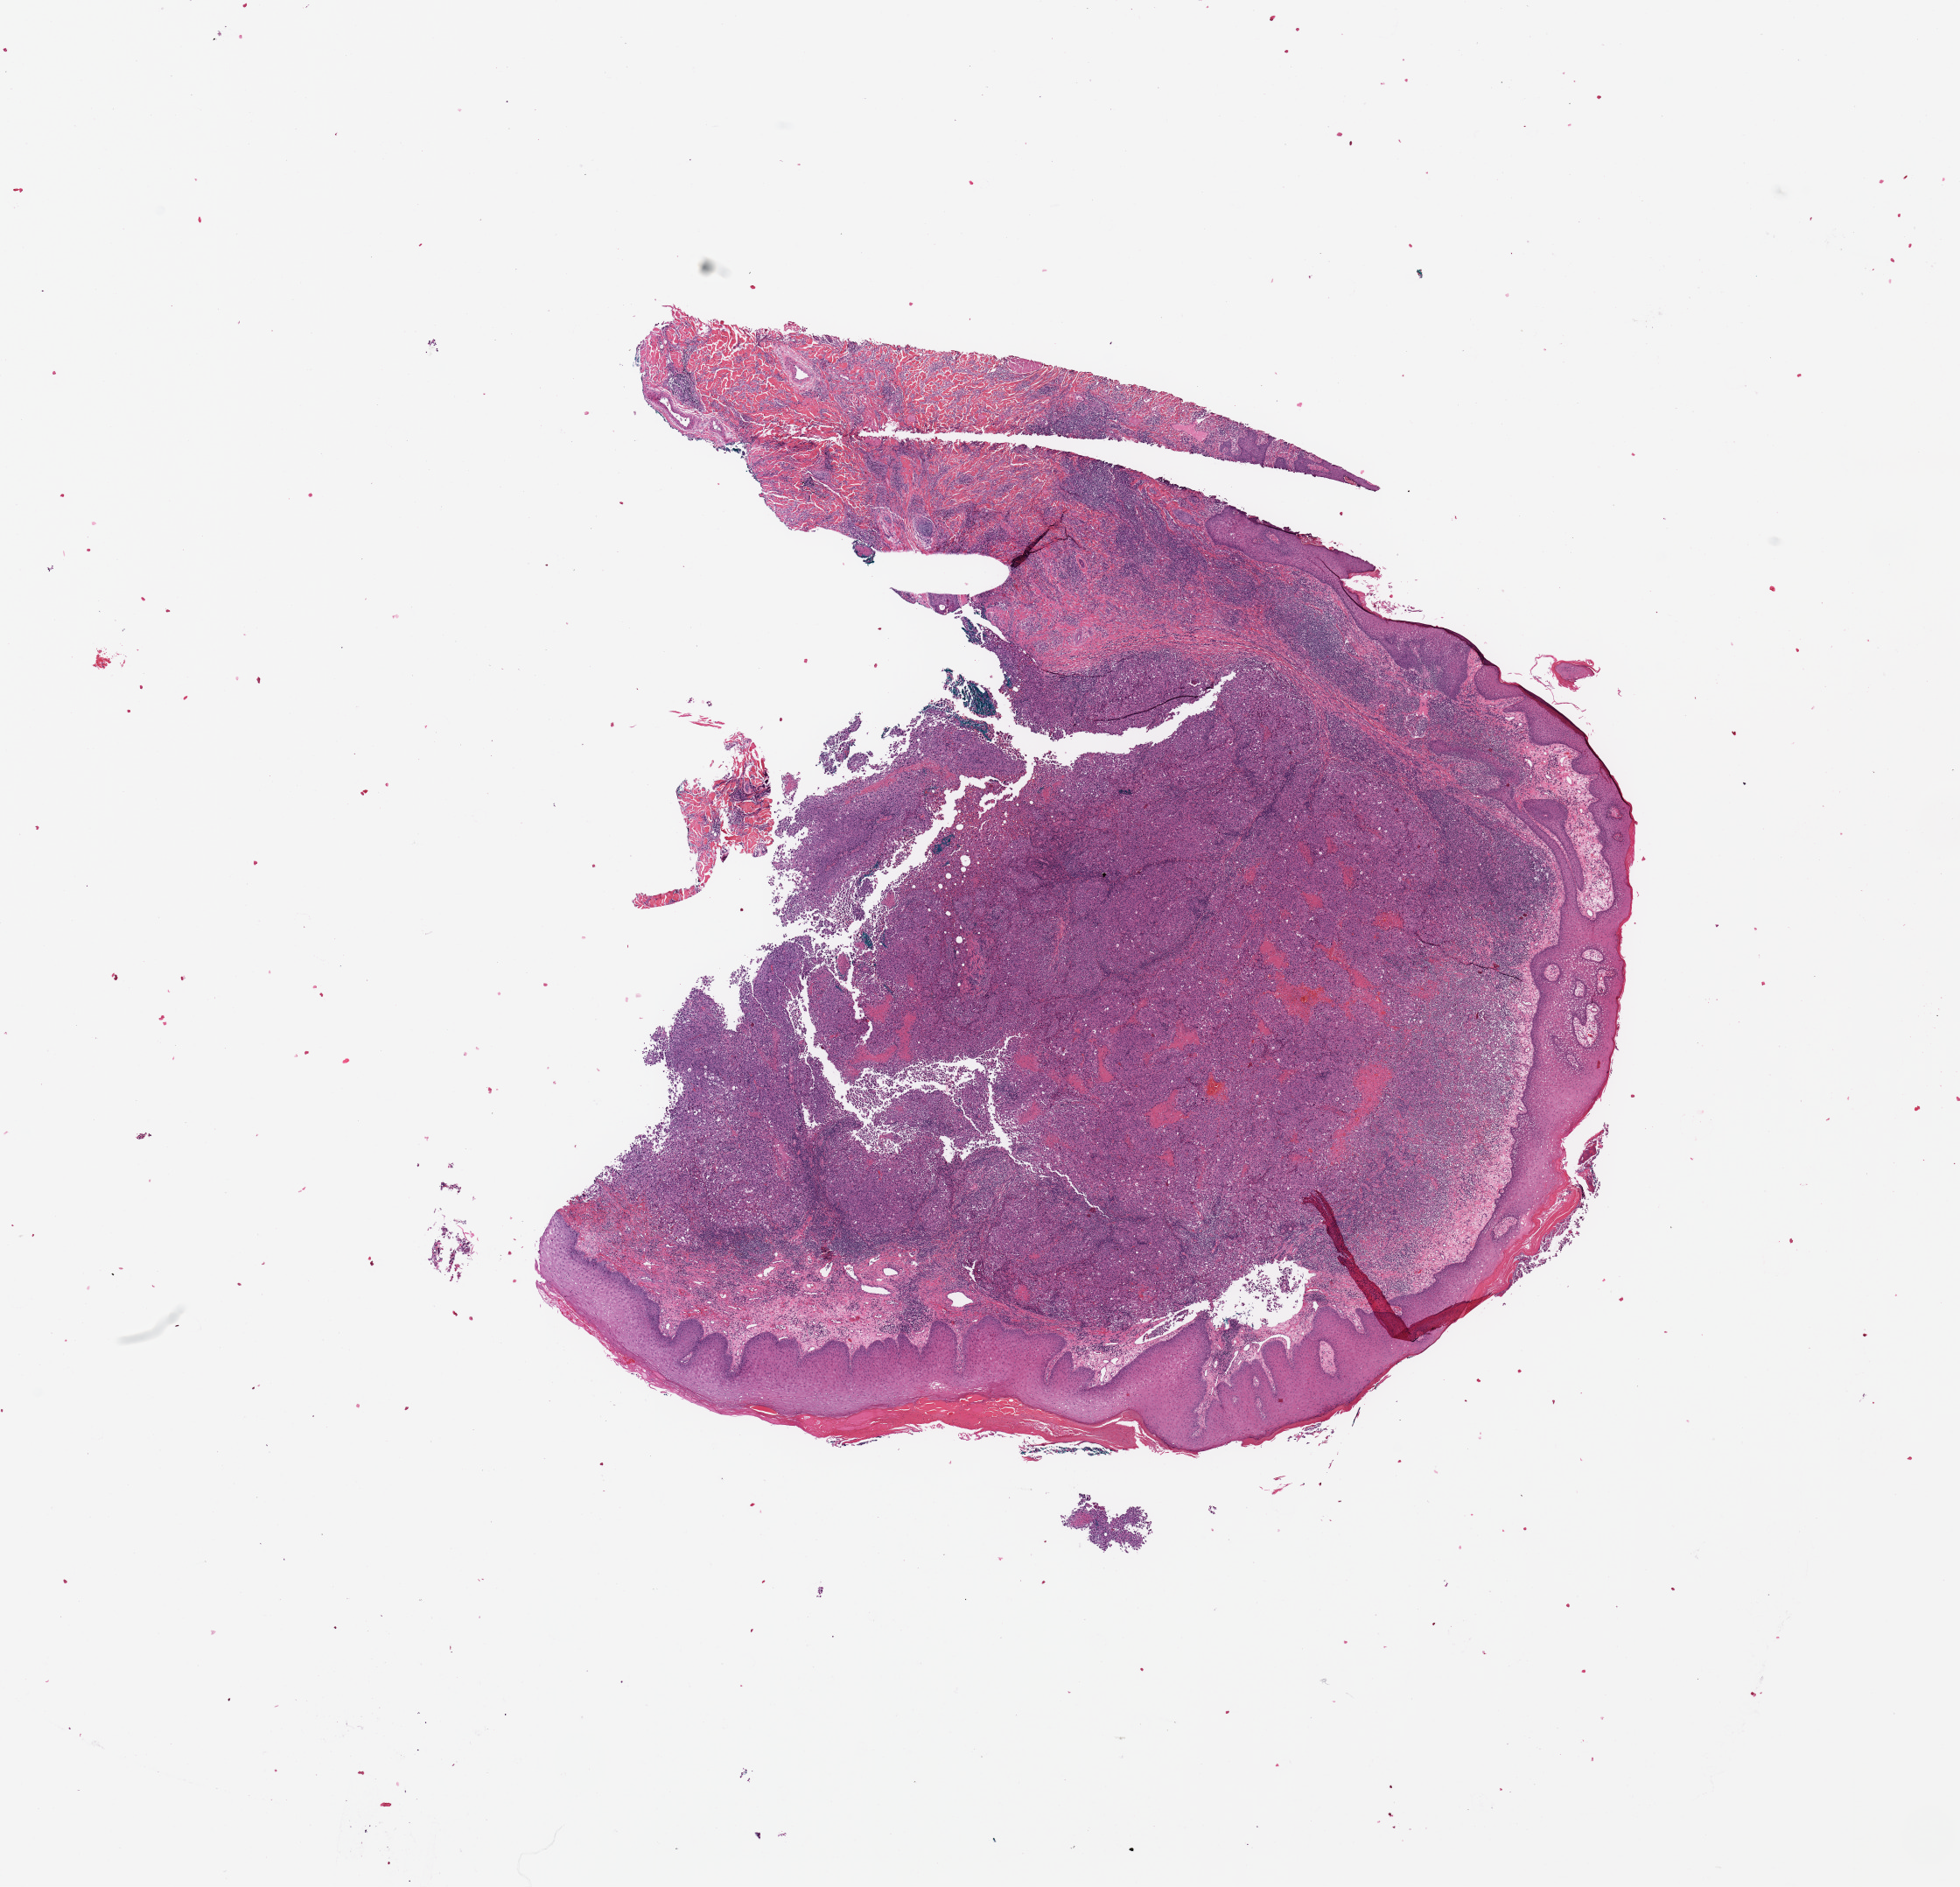
H&E-stained whole-slide image, low-resolution overview of the scanned area, about 17.7 x 17.1 mm (from a 20x scan); melanoma tumour tissue; sampled site not recorded. Patient: male, age 57 years.
Primary tumour site (as recorded): trunk. Histologic diagnosis: Malignant melanoma, NOS. AJCC pathologic stage: IIC.